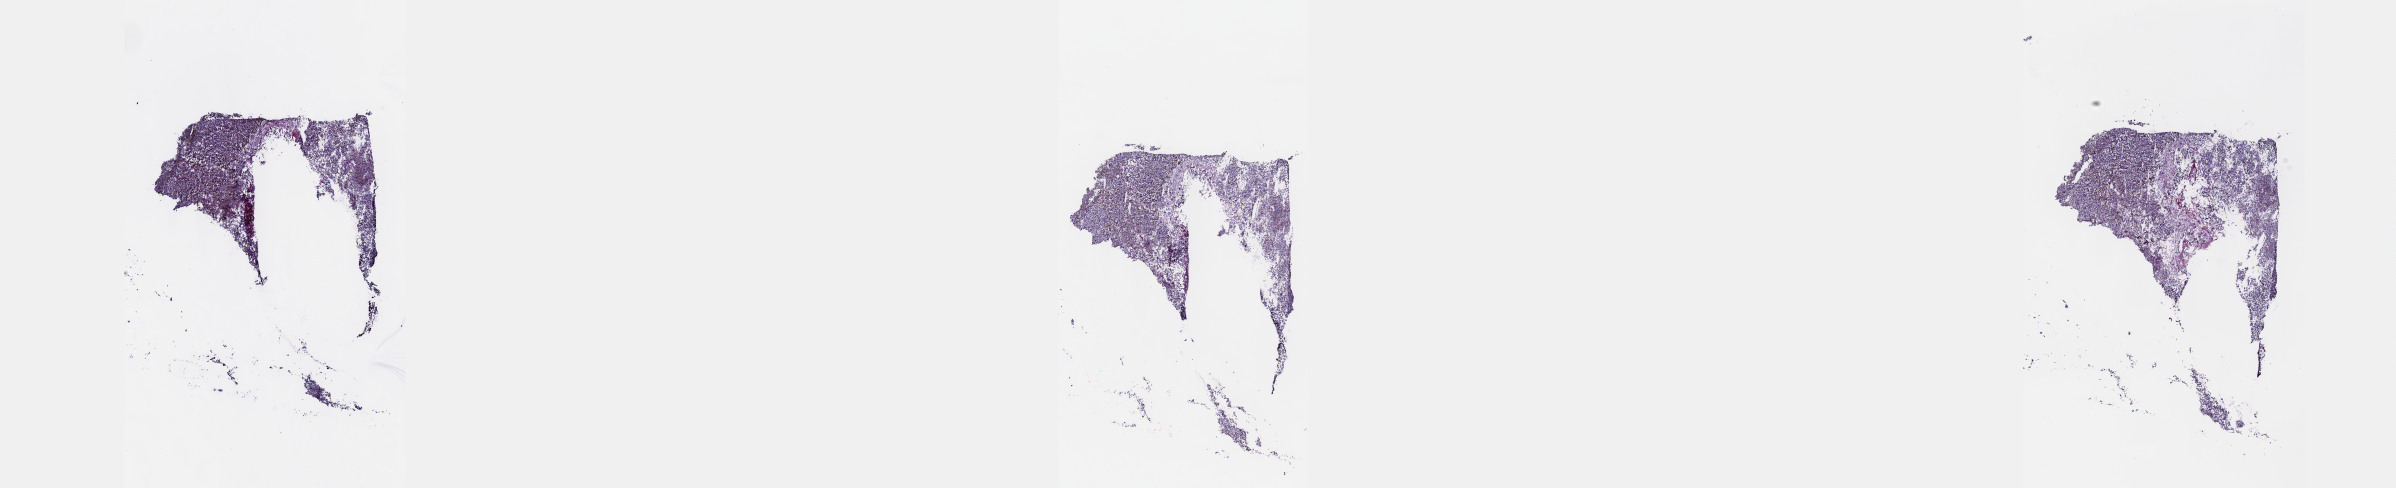
Digitized H&E-stained tissue section (whole slide), shown as a low-resolution overview of the whole scanned area (about 38.7 x 7.9 mm), frozen section from the top of the tissue portion, primary tumour sample from the uvea. Male, age 53 years at initial diagnosis. Slide review estimates, as recorded: tumour cells 95%, tumour nuclei 80%, normal cells 0%, stromal cells 0%, necrosis 5%. Infiltration values recorded for this section: lymphocyte infiltration 2%, monocyte infiltration 0%, neutrophil infiltration 0%.
Diagnosis: Spindle cell melanoma, NOS (choroid). AJCC pathologic stage: IIIB (7th edition).